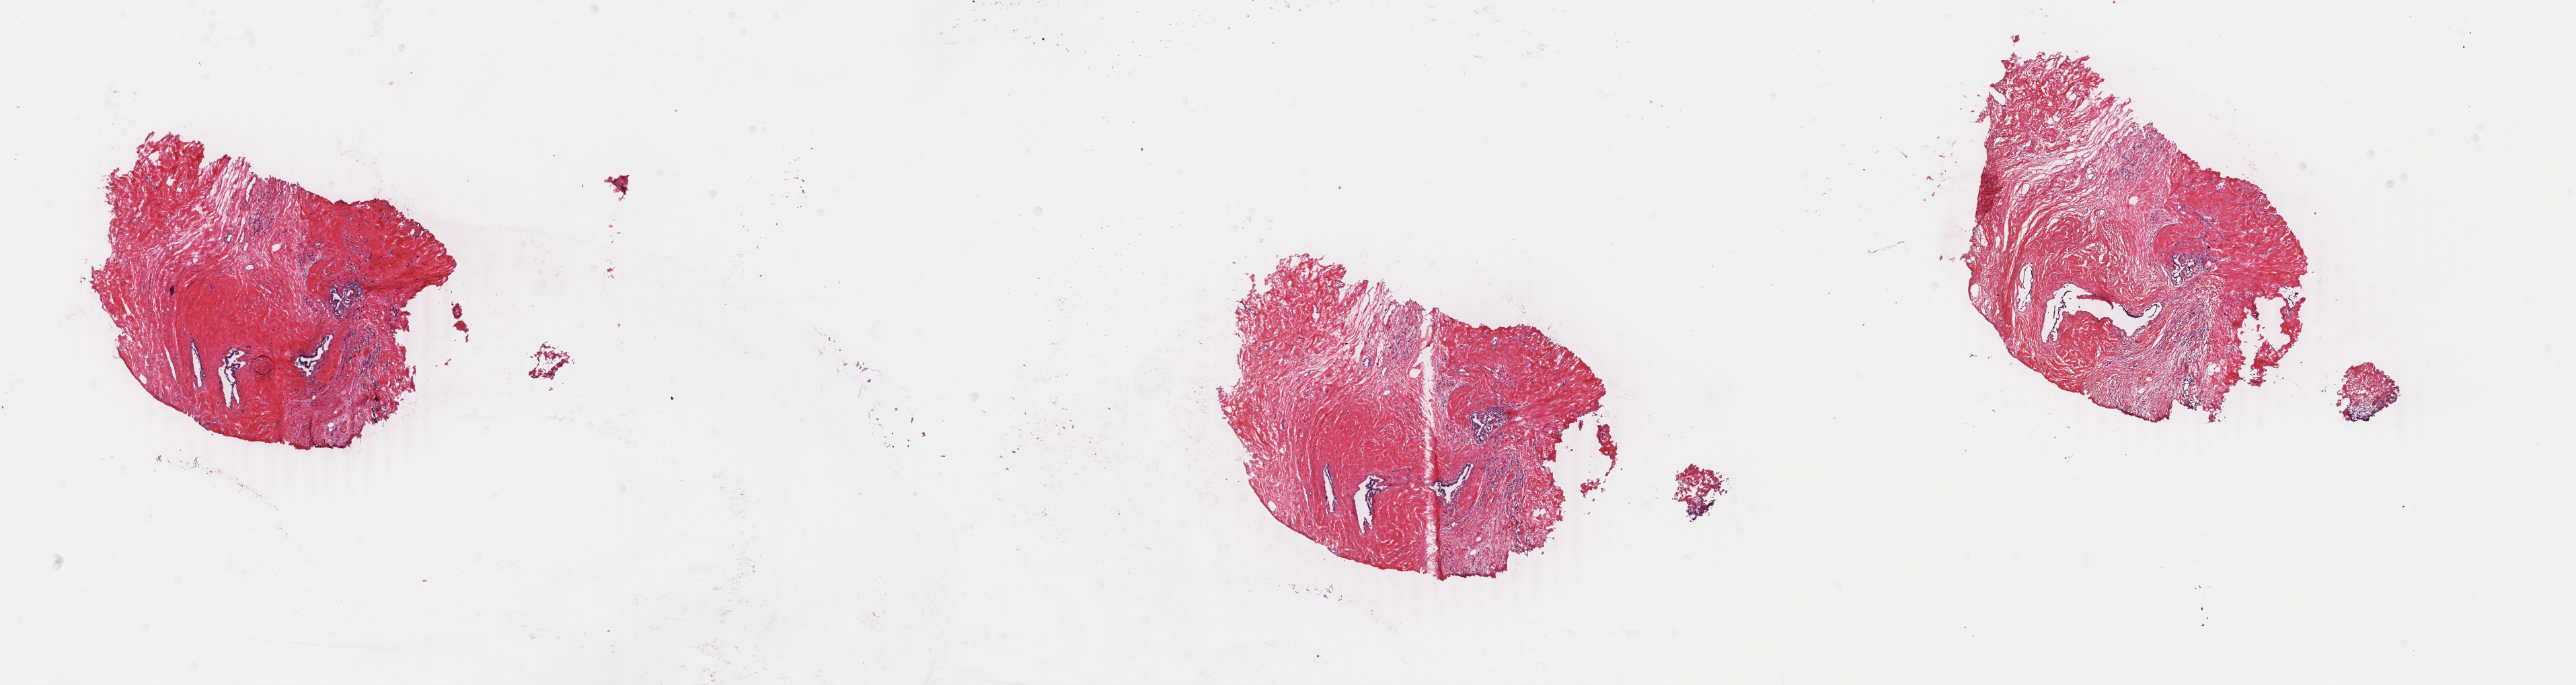
Digitized H&E-stained tissue section (whole slide) — a low-resolution overview of the entire scanned area, about 30.5 x 8.1 mm (from a 40x scan), frozen section from the bottom of the tissue portion, primary tumour sample from the breast. Patient sex: female.
Histologic diagnosis: Lobular carcinoma, NOS.